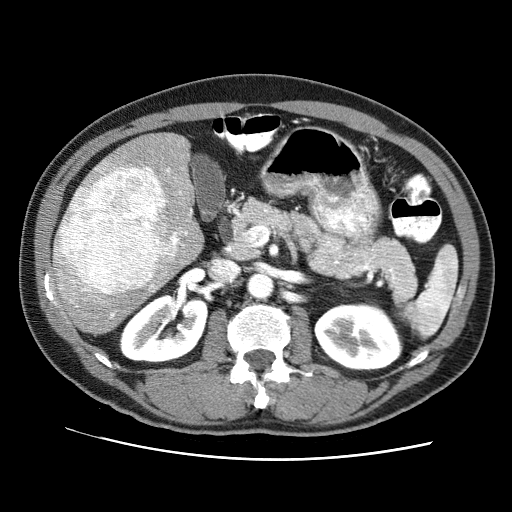
Contrast-enhanced abdominal CT (liver protocol), one axial slice. Slice 37 of 71 in the series (ordered by position). 120 kVp. Soft-tissue window (W 400 / L 40 HU). 2.5 mm slice thickness. 512 × 512 image matrix. From the clinical record (not read from this slice): diagnosis: hepatocellular carcinoma (patient treated with transarterial chemoembolisation; whether this scan precedes or follows treatment is not stated here); TNM stage (as recorded): Stage-II; Child-Pugh class: A.
Structures marked on this image (semi-automatic segmentation, software-assisted and operator-edited):
- liver parenchyma outside the tumour (the mass and vessels are separate outlines, so this box may not span the whole liver): bounding box [x1, y1, x2, y2] px = [53, 131, 204, 333]
- mass: [57, 166, 165, 294]
- liver vessels: [55, 167, 192, 317]